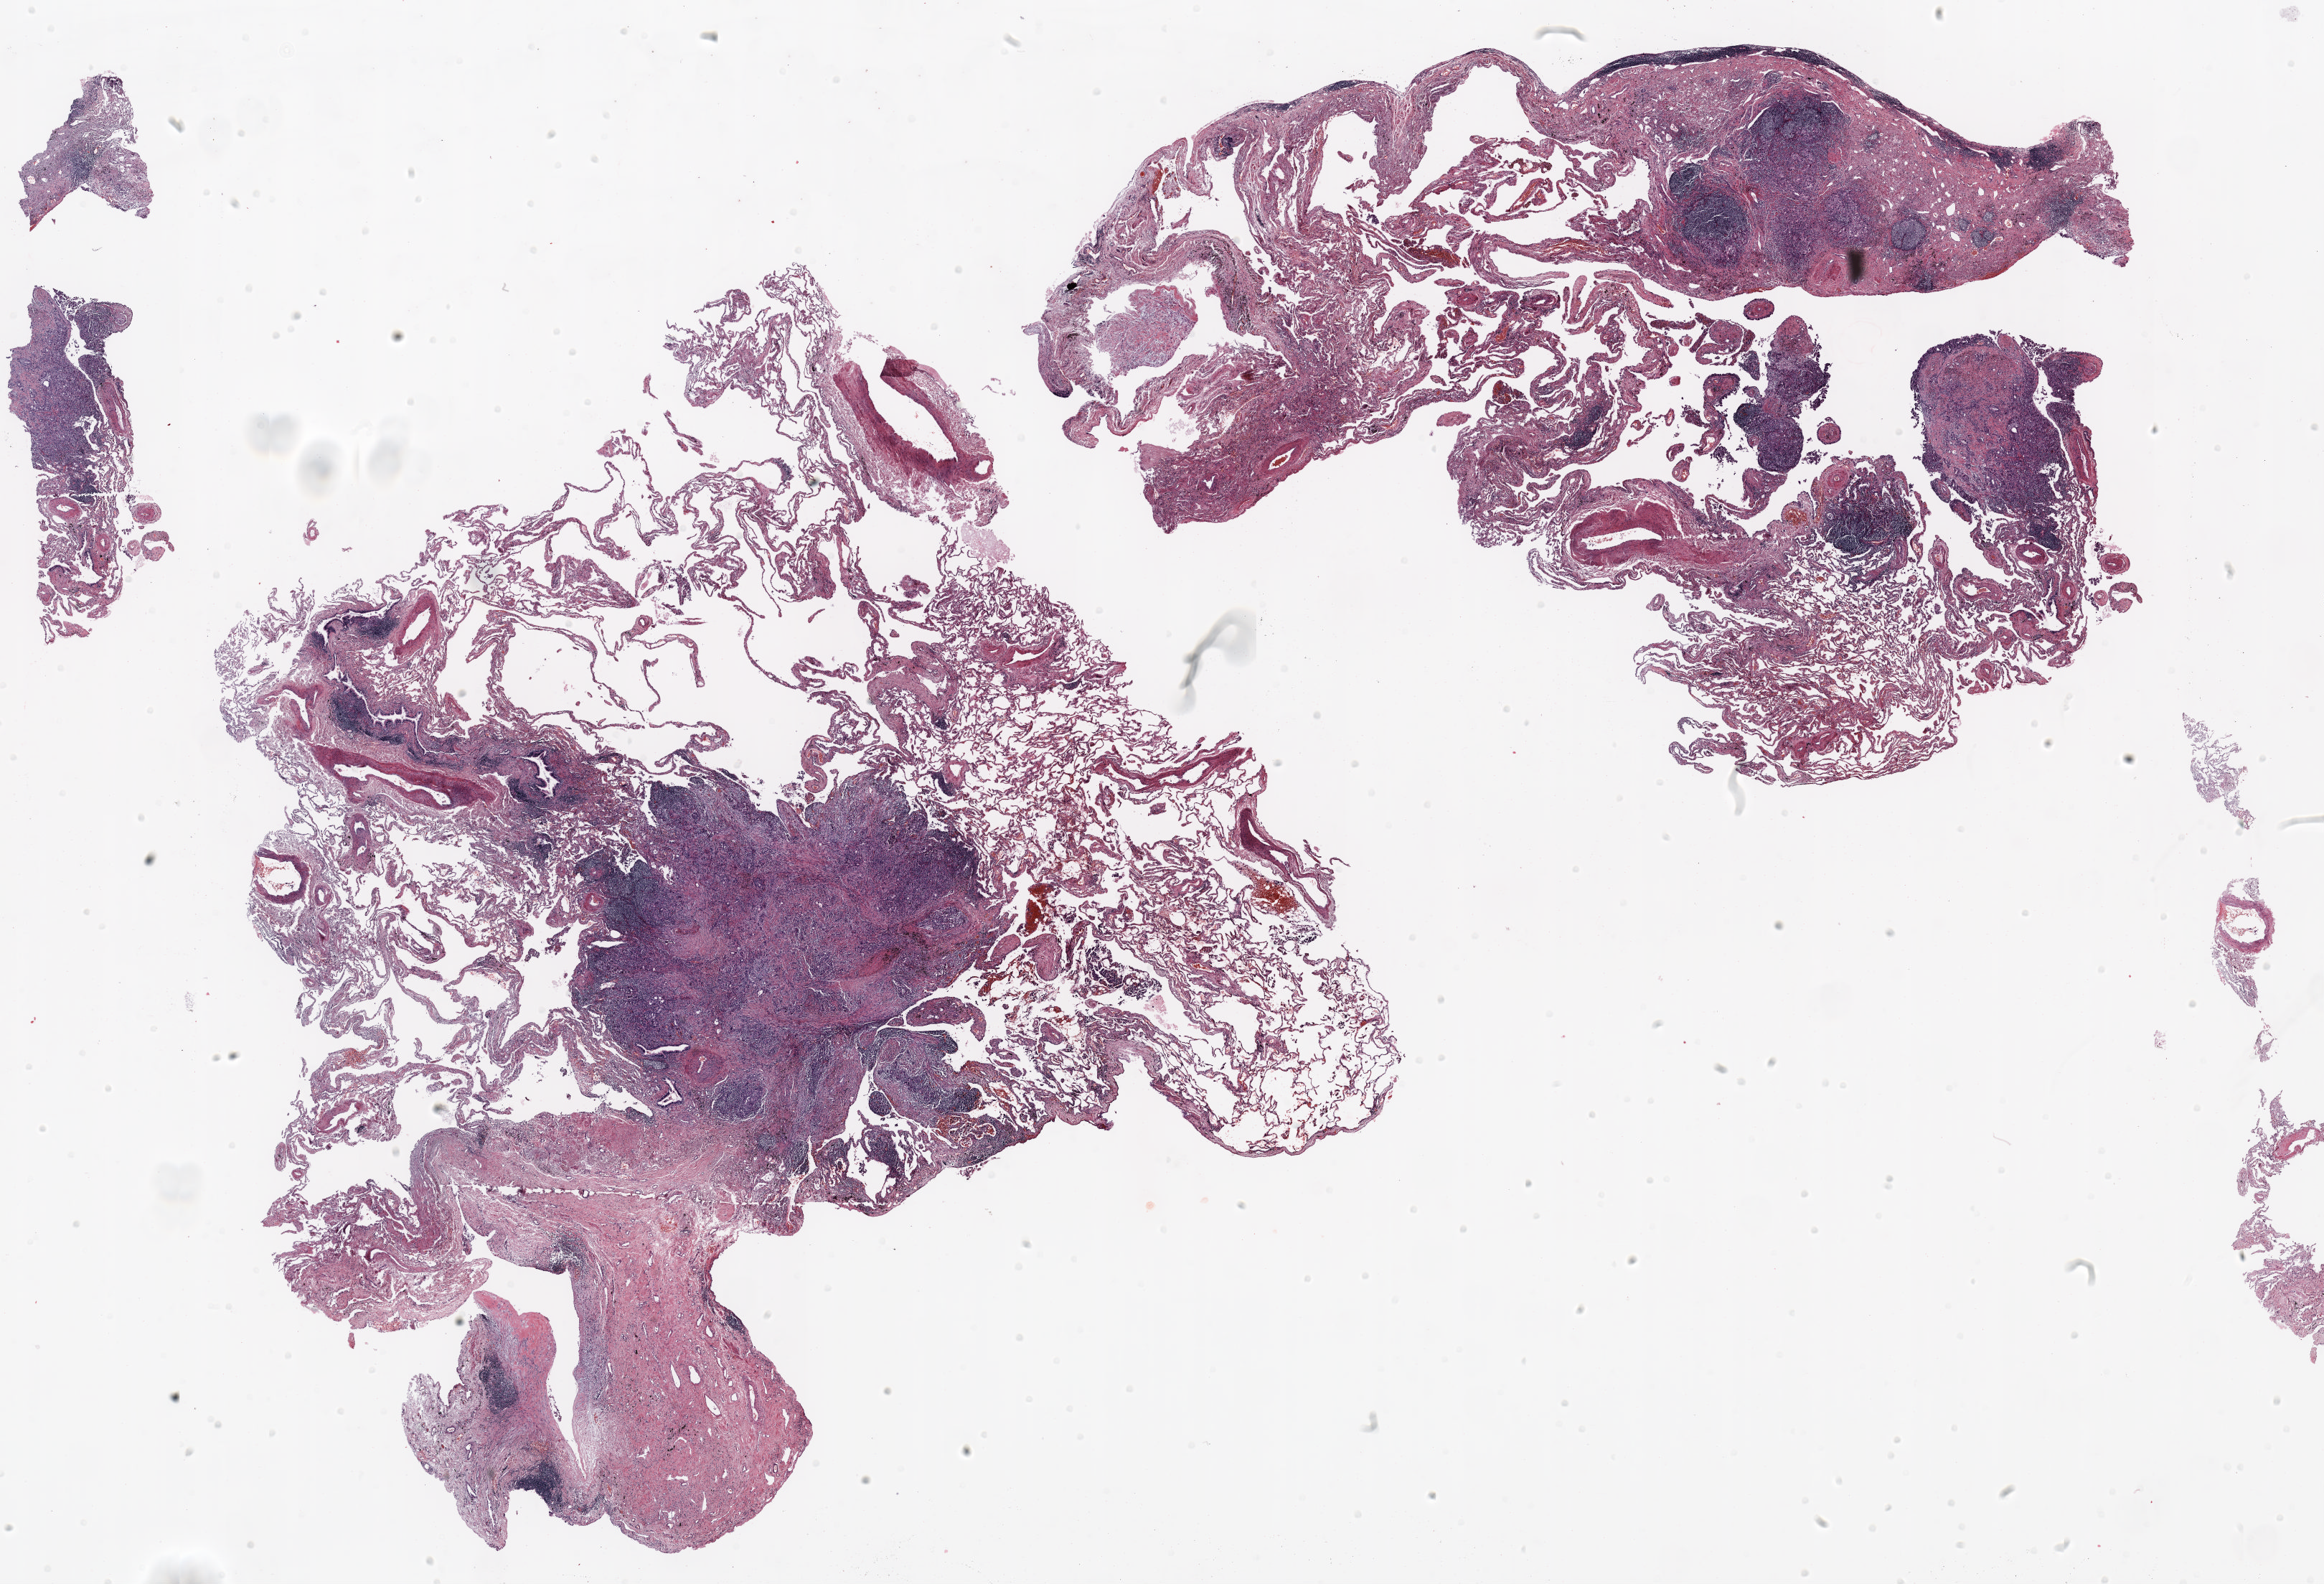
Whole-slide histology image, H&E-stained — whole scanned area (about 26.0 x 17.7 mm) shown as a low-resolution overview. FFPE section. Lung tissue. Male, age 62 at enrolment. Former smoker at enrolment. Grade: moderately differentiated (G2).
• participant's lung-cancer diagnosis: Adenocarcinoma, NOS (ICD-O-3 8140/3)
• primary tumour location (clinical record): left upper lobe
• tumour size (pathology): 10 mm
• stage (AJCC 6th edition): IA